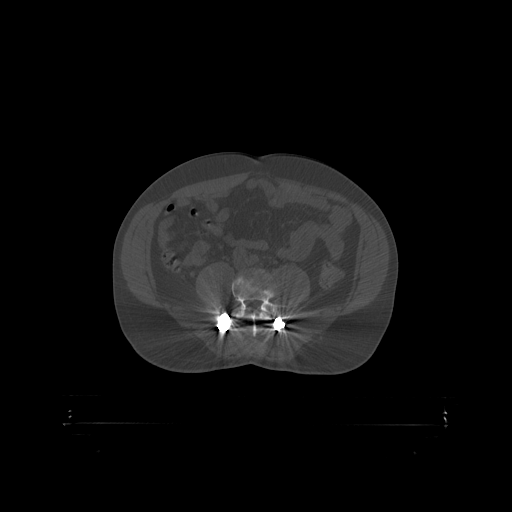
CT including the spine, one axial slice; slice 217 of 399 in the series (ordered by position); bone window (W 1800 / L 400 HU); 1.25 mm slice thickness; 512 × 512 image matrix, field of view 650 × 650 mm. Patient: male, 46 years. Case-level facts recorded for this patient, not image findings: primary cancer: skin.
Structures marked on this image (semi-automatic segmentation, software-assisted and operator-edited):
- L4 vertebra: bounding box [x1, y1, x2, y2] px = [235, 312, 271, 319]
- L5 vertebra: [232, 275, 281, 319]